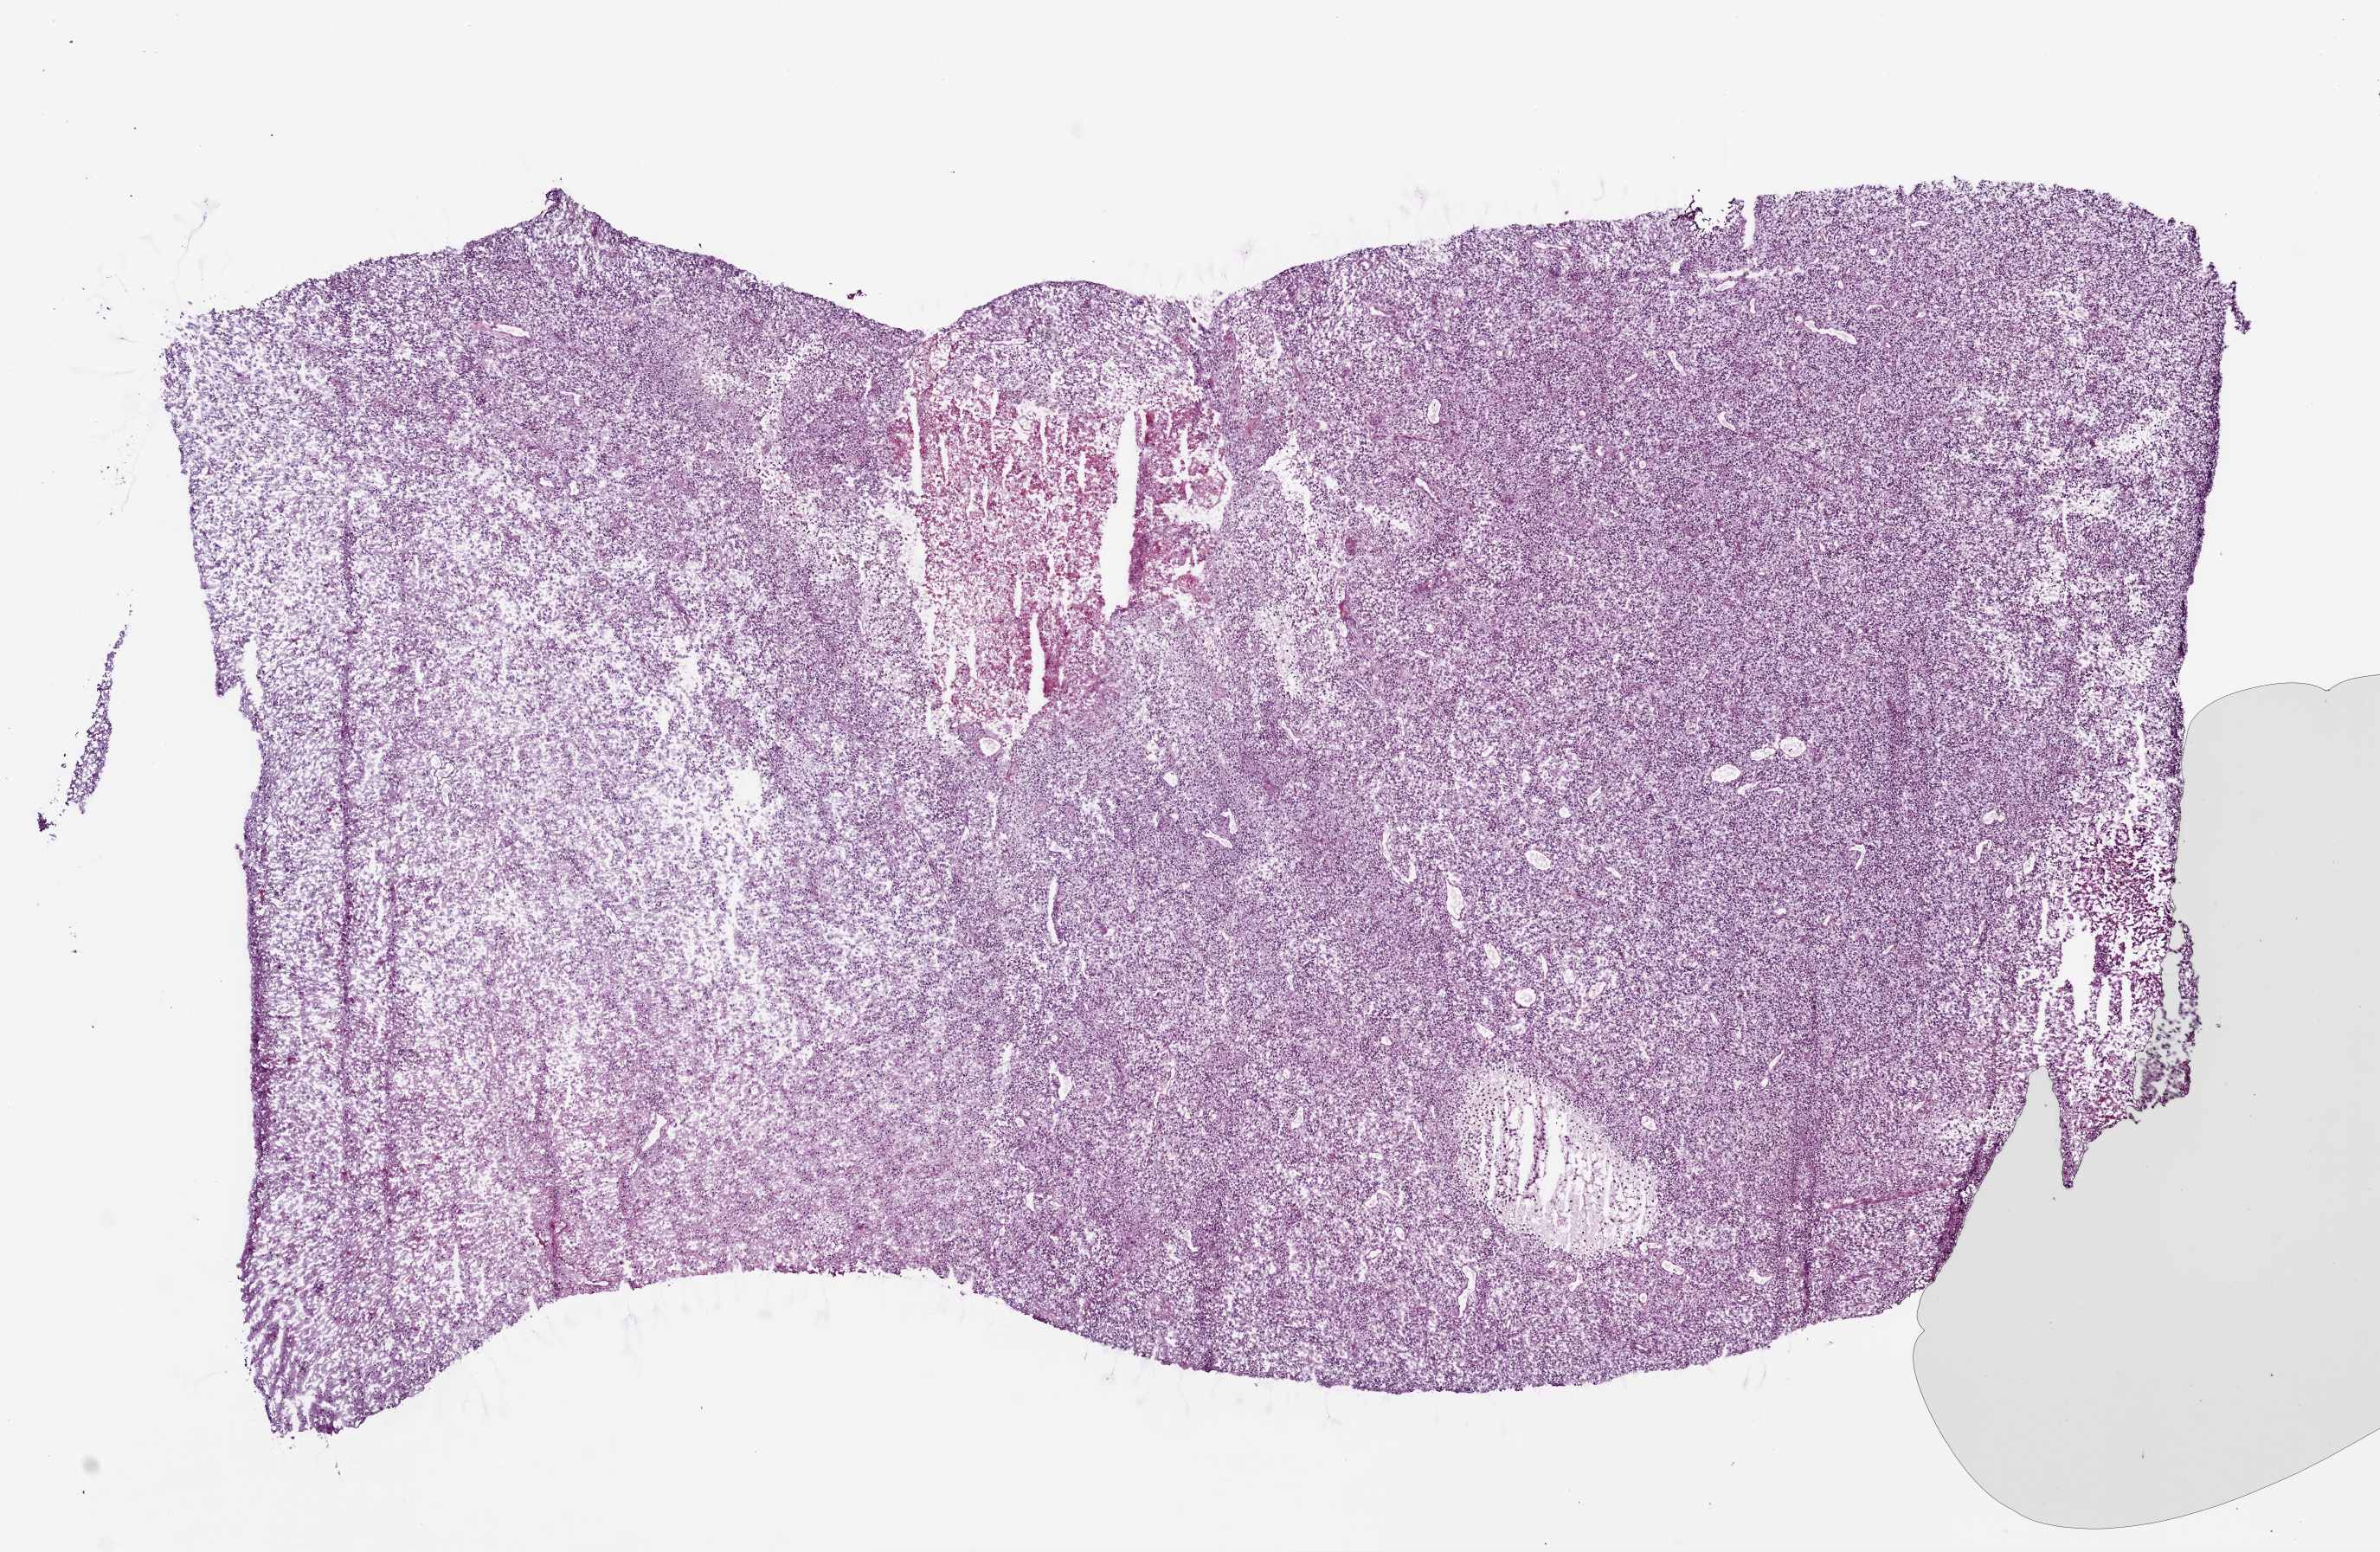
Whole-slide histology image, Hematoxylin and eosin (H&E) stained — low-resolution overview of the scanned area, about 11.0 x 7.2 mm, frozen section, brain, primary tumour sample. Male patient; age at initial diagnosis 52 years. Pathologist review of this section (percent, as recorded): tumour cells 90%, tumour nuclei 85%, normal cells 0%, stromal cells 0%, necrosis 10%.
* histologic diagnosis: Glioblastoma